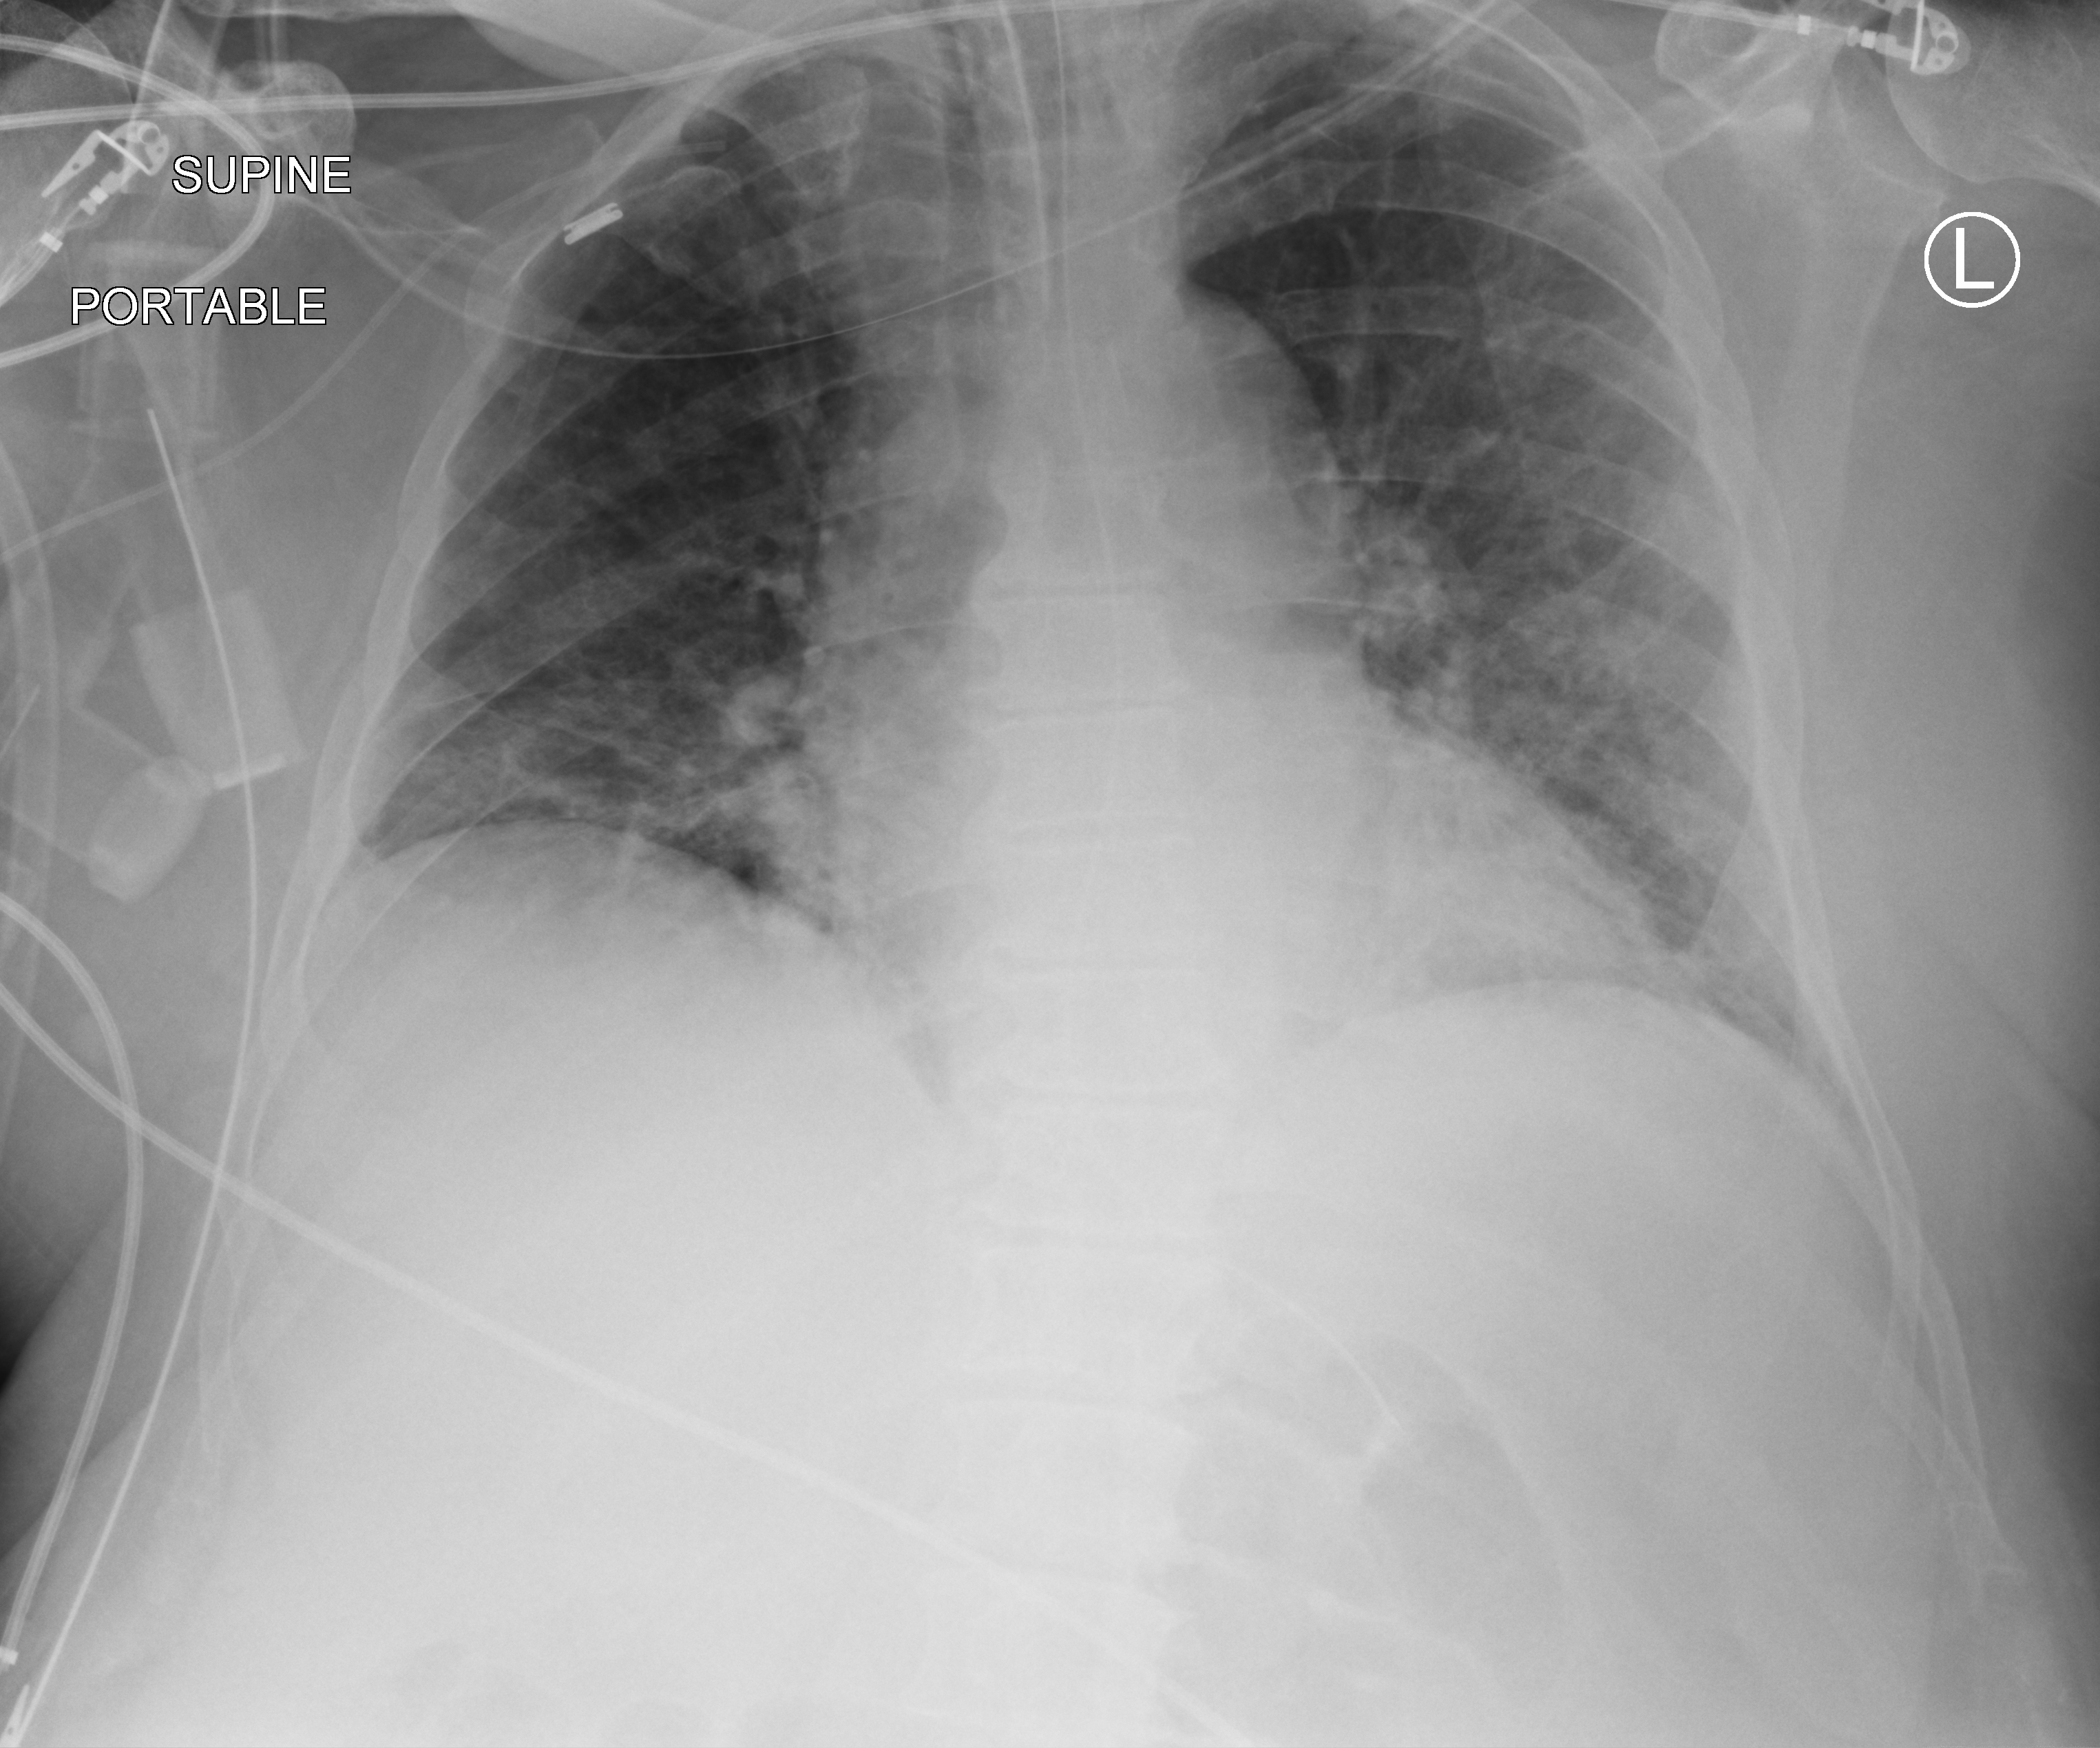
Chest X-ray (portable), anteroposterior (AP) projection. Patient hospitalised with COVID-19; male, aged 60–74 years.
Admission-level facts for this patient (not findings on this image; timing relative to this image not recorded):
- admitted to intensive care during this hospital stay: yes
- other chronic lung disease (admission record): no